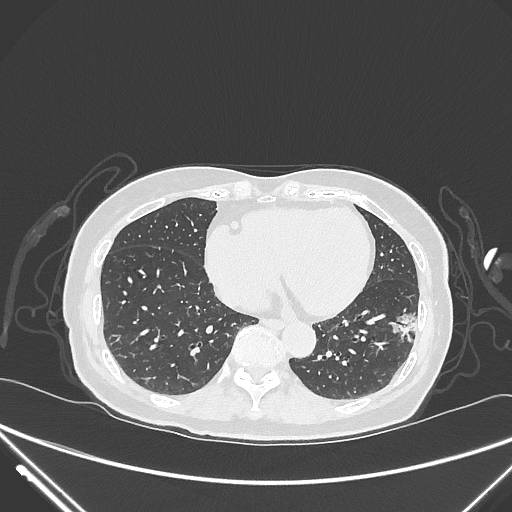
Chest CT, one axial slice; reconstruction kernel IMR1,SharpPlus; 120 kVp; lung window (W 1500 / L -600 HU); 1 mm slice thickness; 512 × 512 image matrix, field of view 377 × 377 mm. Patient: female, 82 years. Case-level facts recorded for this patient, not image findings: clinical TNM (as recorded): T1c N0 M0; histopathological grade: G2.
Outlined on this slice (bounding box drawn by a radiologist):
- lung tumour (recorded histology: adenocarcinoma): bounding box [x1, y1, x2, y2] px = [394, 301, 426, 348]